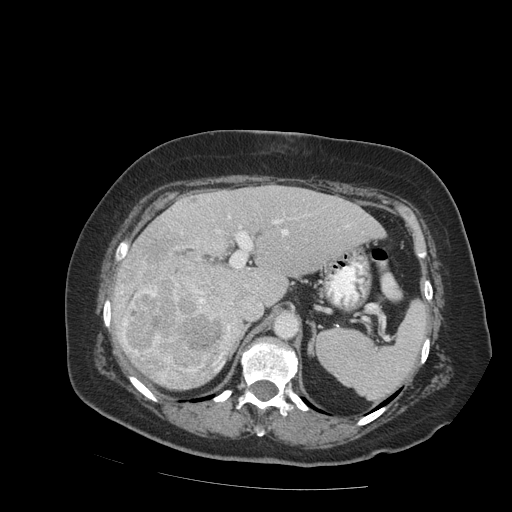
Contrast-enhanced abdominal CT (liver protocol), one axial slice. Position 54 of 99 along the scan axis. 140 kVp. Soft-tissue window (W 400 / L 40 HU). 2.5 mm slice thickness. 512 × 512 image matrix, field of view 400 × 400 mm. Case-level facts recorded for this patient, not image findings: diagnosis: hepatocellular carcinoma (patient treated with transarterial chemoembolisation; whether this scan precedes or follows treatment is not stated here); TNM stage (as recorded): Stage-IVB; Child-Pugh class: A; tumour differentiation: moderately differentiated.
Annotated regions visible in this slice (semi-automatic segmentation, software-assisted and operator-edited):
- liver parenchyma outside the tumour (the mass and vessels are separate outlines, so this box may not span the whole liver): bounding box <112,184,384,388> (left, top, right, bottom; pixels)
- mass: <113,225,235,388>
- liver vessels: <217,216,289,287>